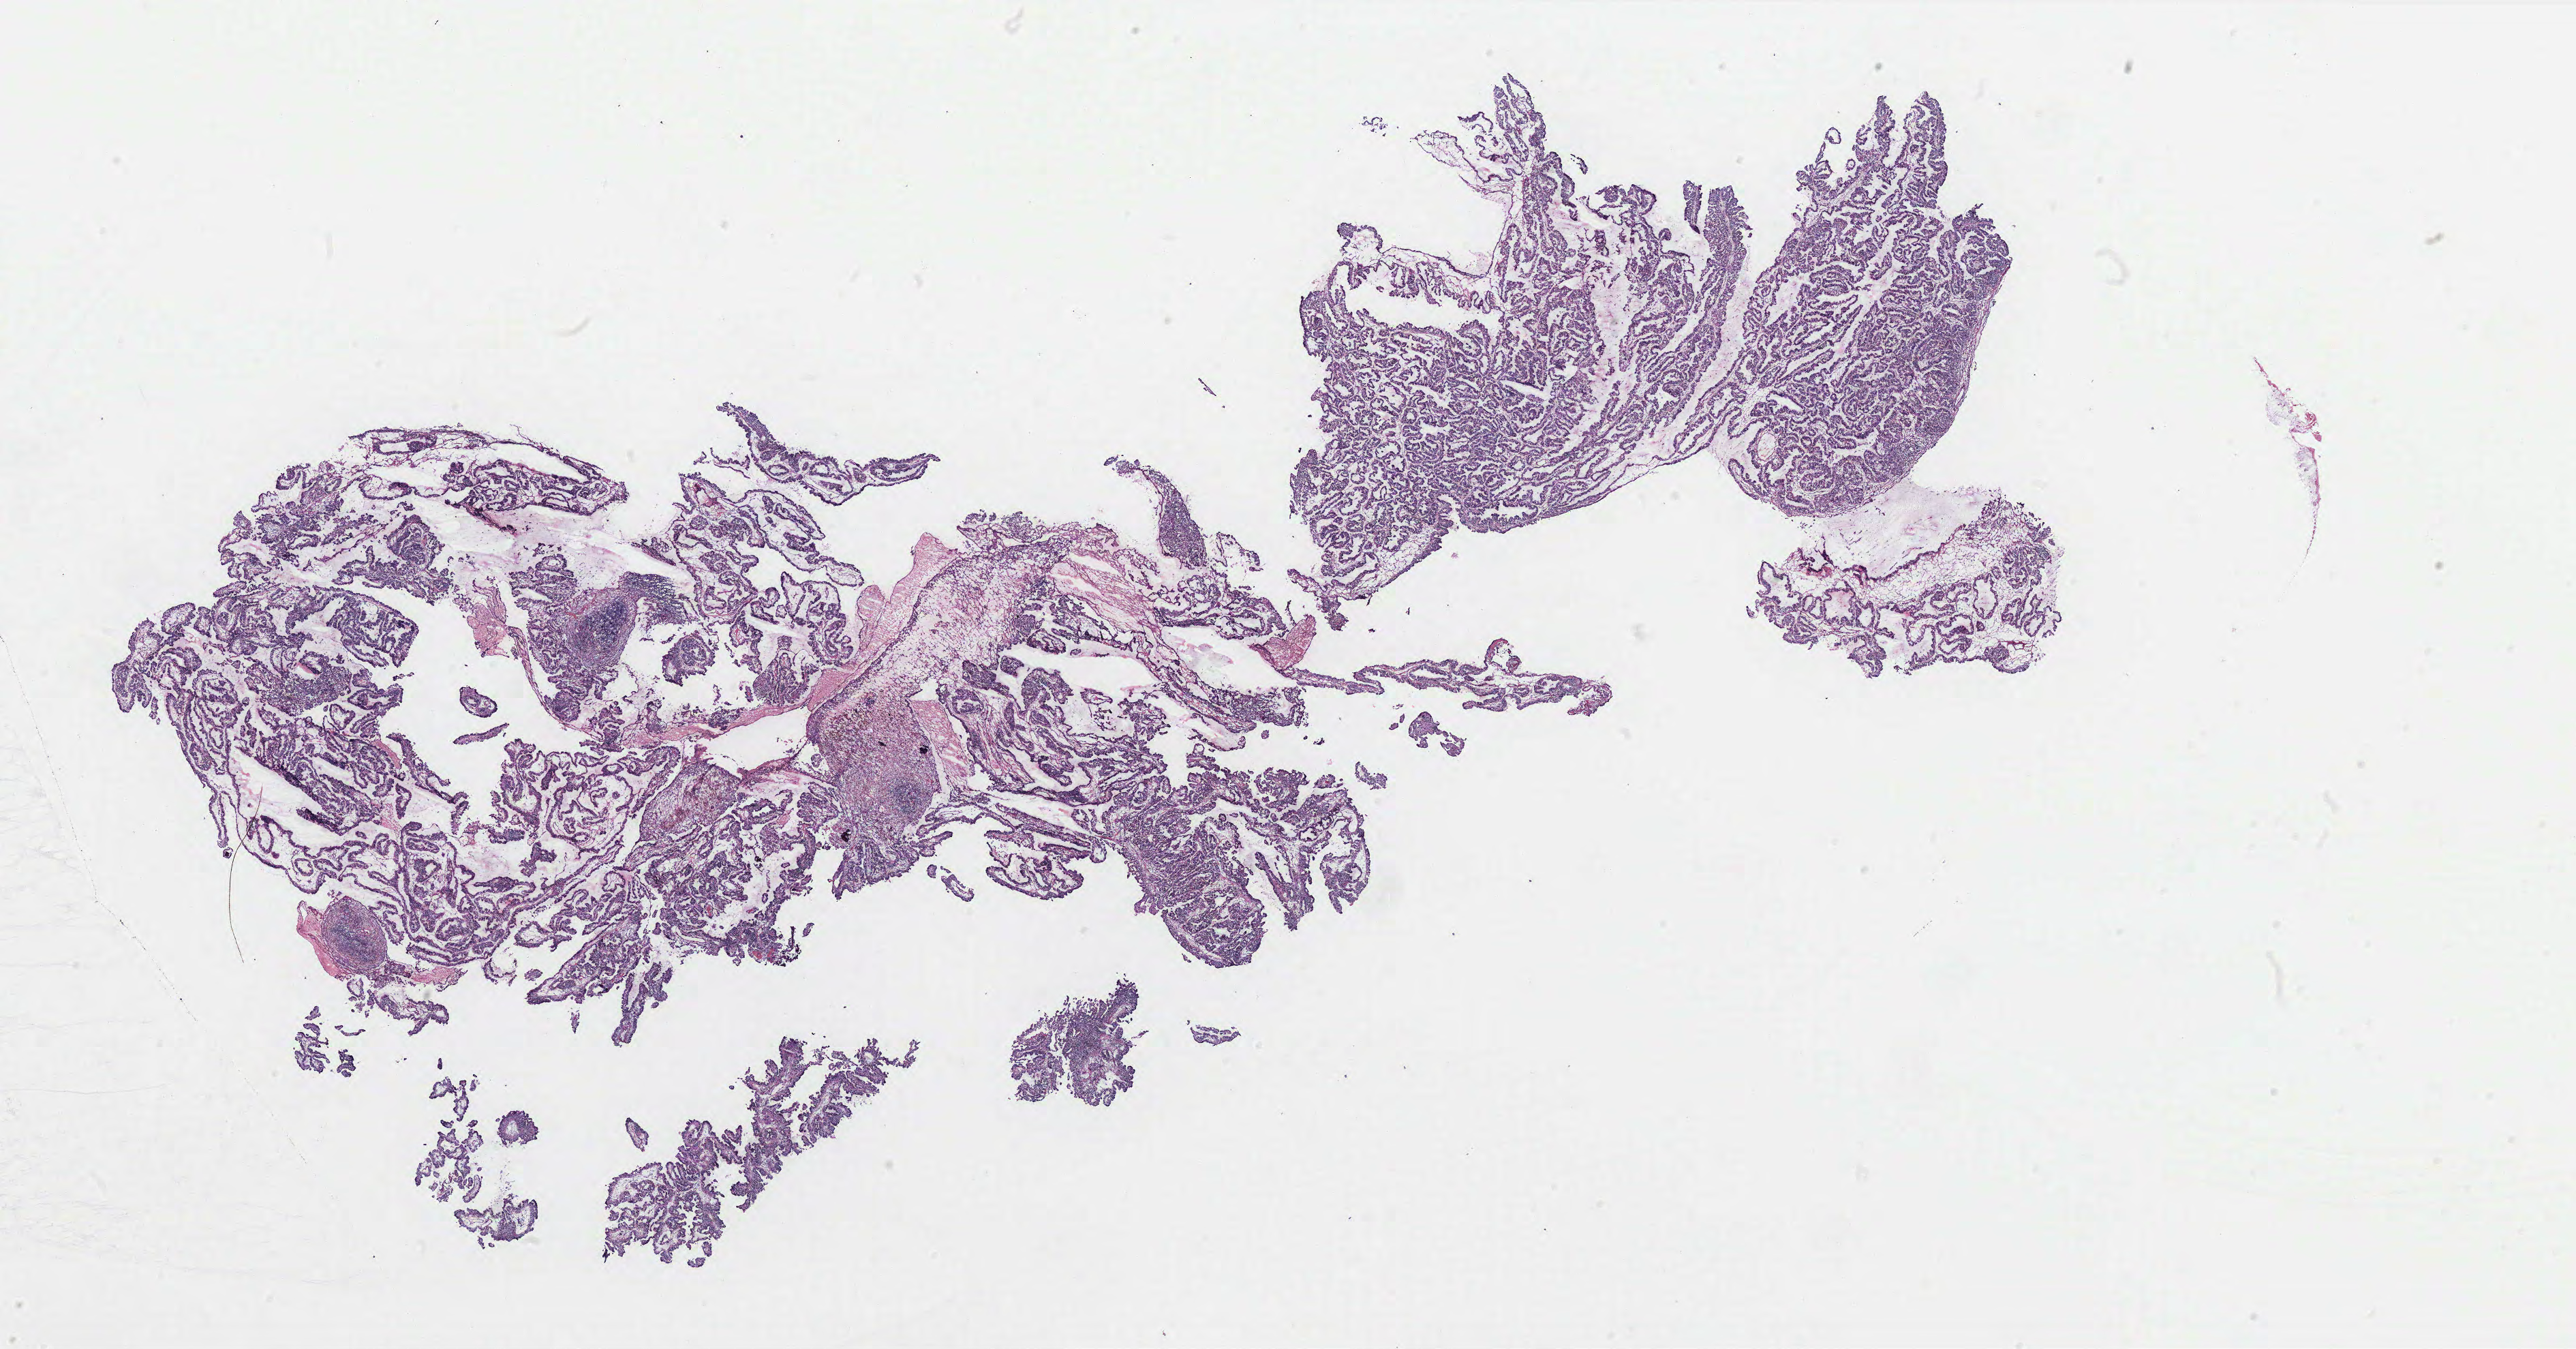
Digitized H&E-stained tissue section (whole slide) — shown as a low-resolution overview of the whole scanned area (about 30.3 x 15.8 mm). Normal (non-tumour) tissue sample, ovary. Female, 56 y/o.
This section: normal (non-tumour) tissue from the same patient. Patient diagnosis: Serous adenocarcinoma, NOS.